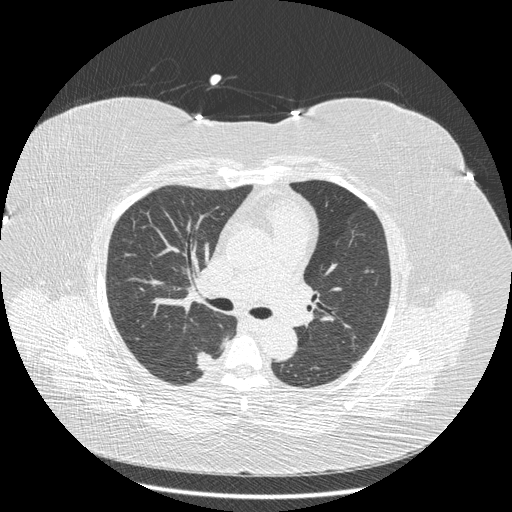
Chest CT (low-dose screening protocol), one axial image; first (baseline) screen; lung window (W 1500 / L -600 HU); 1.25 mm slice thickness; 120 kVp; slice 80 of 211 in the series; 512 × 512 image matrix. Female, age 58 years at enrolment. Current smoker at enrolment.
• Expert reader's lesion annotation, bounding box (x1, y1, x2, y2) in pixels: (185, 345, 226, 382).
• Screening reader's record for this exam (one nodule recorded; not confirmed to be the boxed lesion): non-calcified nodule or mass ≥4 mm, right lower lobe, 15 × 10 mm, smooth margins, soft tissue attenuation.
• Official screen result: positive, change unspecified: nodule(s) >= 4 mm or enlarging nodule(s), mass(es), or other non-specific abnormalities suspicious for lung cancer.
• Lung cancer was diagnosed 362 days after this screen: adenocarcinoma, NOS, right lower lobe, stage IB (AJCC 6th edition), 15 mm at pathology.